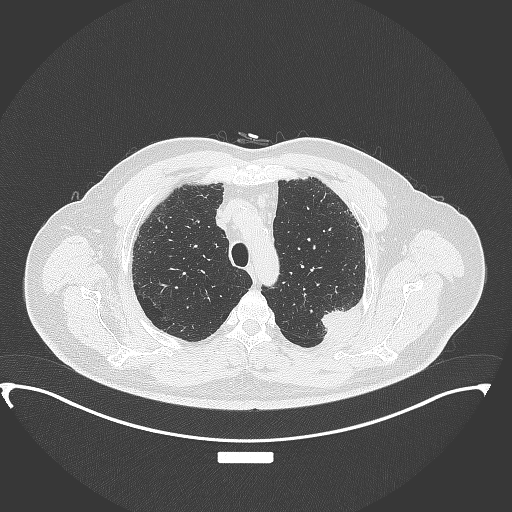
Chest CT, one axial slice. Slice 285 of 350 in the series (ordered by position). Reconstruction kernel B70f. 120 kVp. Lung window (W 1500 / L -600 HU). 512 × 512 image matrix, field of view 459 × 459 mm. Patient: male, 64 years. Case-level facts recorded for this patient, not image findings: clinical TNM (as recorded): T1c N1 M1.
Structures marked on this image (rectangle marked by the reading radiologist):
- lung tumour (recorded histology: adenocarcinoma): box from (x=318, y=301) to (x=359, y=347) px